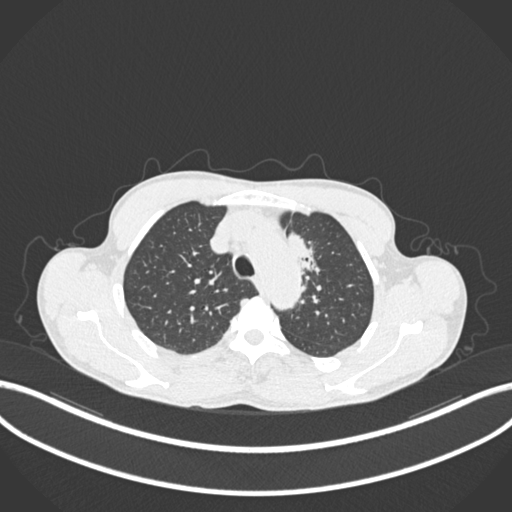
Chest CT, one axial slice; position 157 of 211 along the scan axis; reconstruction kernel B30f; lung window (W 1500 / L -600 HU); 512 × 512 image matrix. Male patient, age 58 years. Case-level facts recorded for this patient, not image findings: clinical TNM (as recorded): T1c N1 M0.
Annotated regions visible in this slice (bounding box drawn by a radiologist):
- lung tumour (recorded histology: adenocarcinoma): bounding box (x1, y1, x2, y2) in pixels: (286, 224, 322, 278)